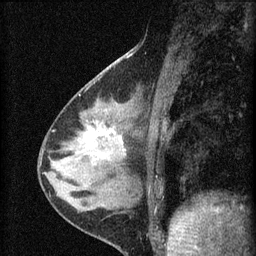
Breast MRI (dynamic contrast-enhanced), one sagittal slice; position 23 of 60 along the scan axis; dynamic contrast-enhanced series, image 2 of 4 at this slice position (ordered by acquisition); 1.5 T; TE 4.2 ms, TR 8.2 ms; 2 mm slice thickness; 256 × 256 image matrix, field of view 180 × 180 mm. Patient: female, 37 years.
Structures marked on this image (semi-automatic segmentation, software-assisted and operator-edited):
- analysis volume of interest (the breast-tissue region the enhancement analysis was run in; not a lesion): bounding box <77,116,127,175> (left, top, right, bottom; pixels)
- tumour enhancement mask (voxels above the 70 % enhancement threshold inside the analysis volume of interest): <88,128,123,144>